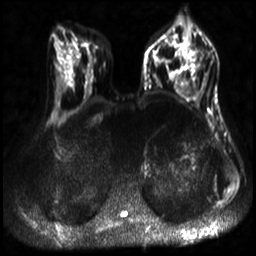
Breast MRI, one axial slice. Position 11 of 30 along the scan axis. Diffusion-weighted series; image 2 of 4 stored at this slice position (different b-values; order by instance number). 3 T. 4 mm slice thickness. 256 × 256 image matrix, field of view 320 × 320 mm. Female patient.
Structures marked on this image (expert manual segmentation):
- tumour on diffusion-weighted imaging: bounding box <192,46,197,51> (left, top, right, bottom; pixels)